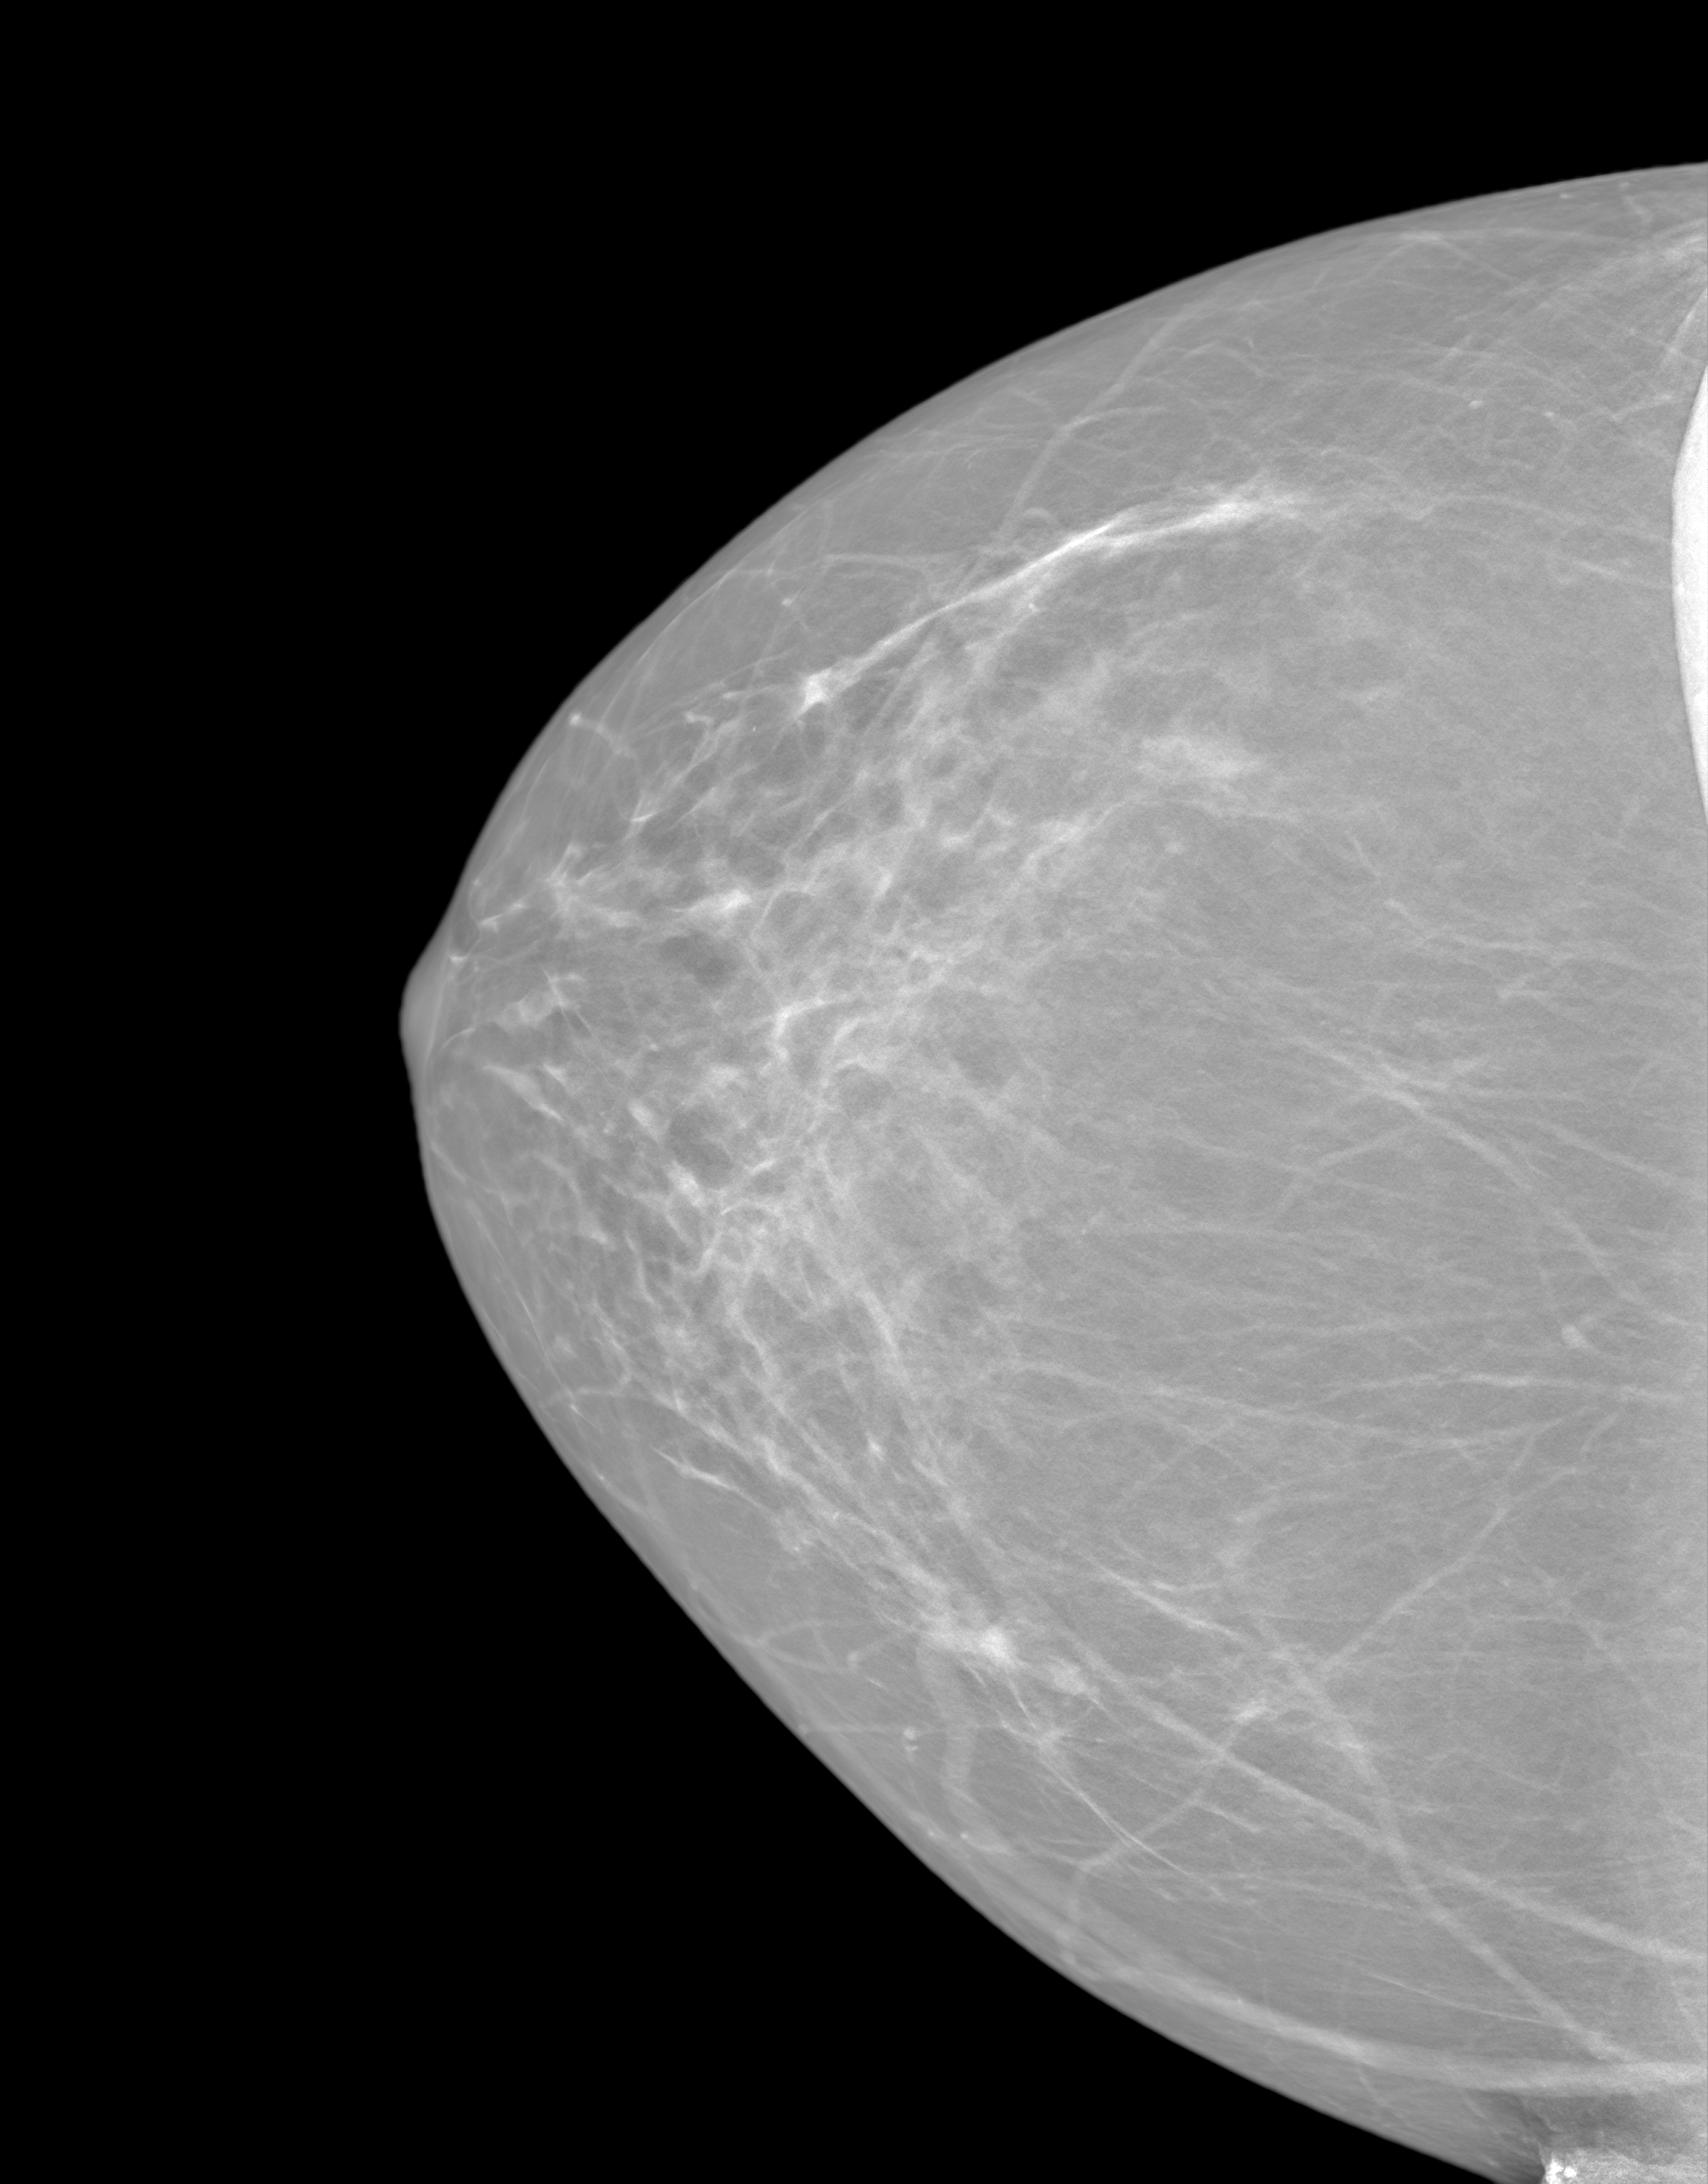
Screening examination. Patient: female, 59 years.
Image type: synthesized 2-D view from tomosynthesis. Breast: right. Projection: cranio-caudal projection.